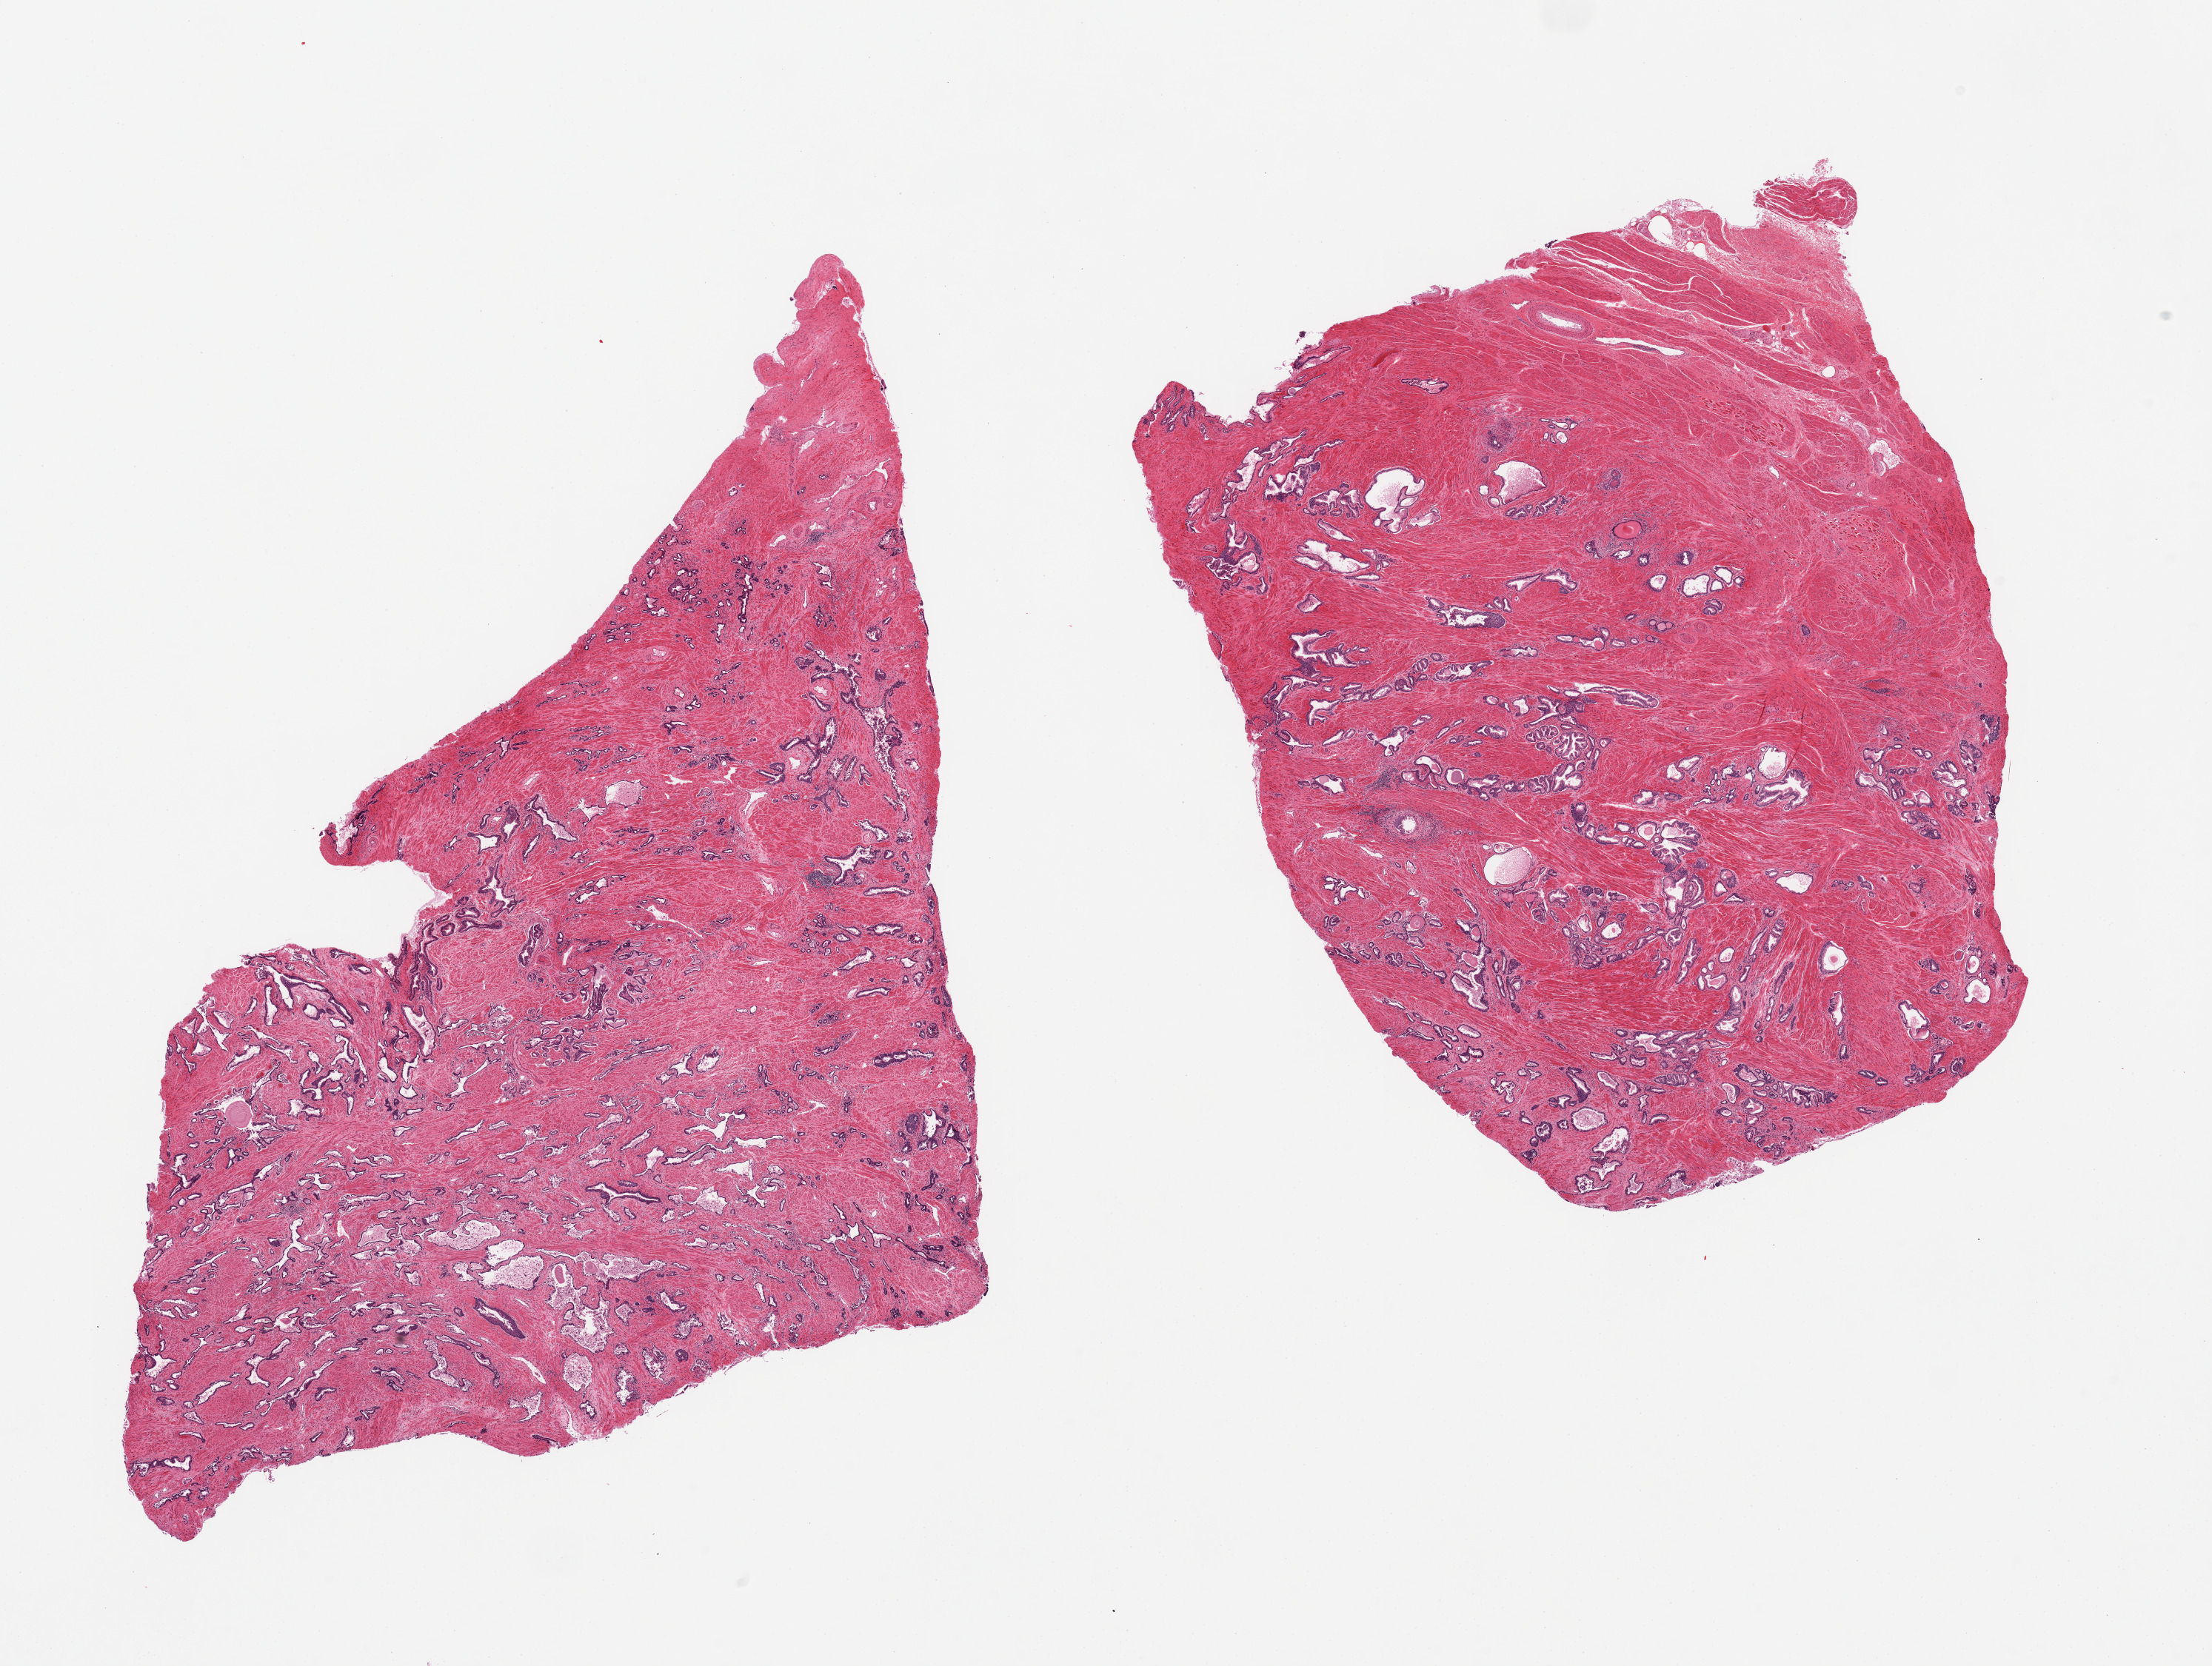
Whole-slide image, H&E stain, brightfield — whole scanned area (about 23.6 x 17.8 mm) shown as a low-resolution overview. PAXgene-fixed, paraffin-embedded tissue. Target tissue: prostate. Tissue donor sample. Donor sex: male.
• review note (as recorded): 2 piecesm hyperplastic glandular pattern; glandular epithelium moderately/markedly autolyzed